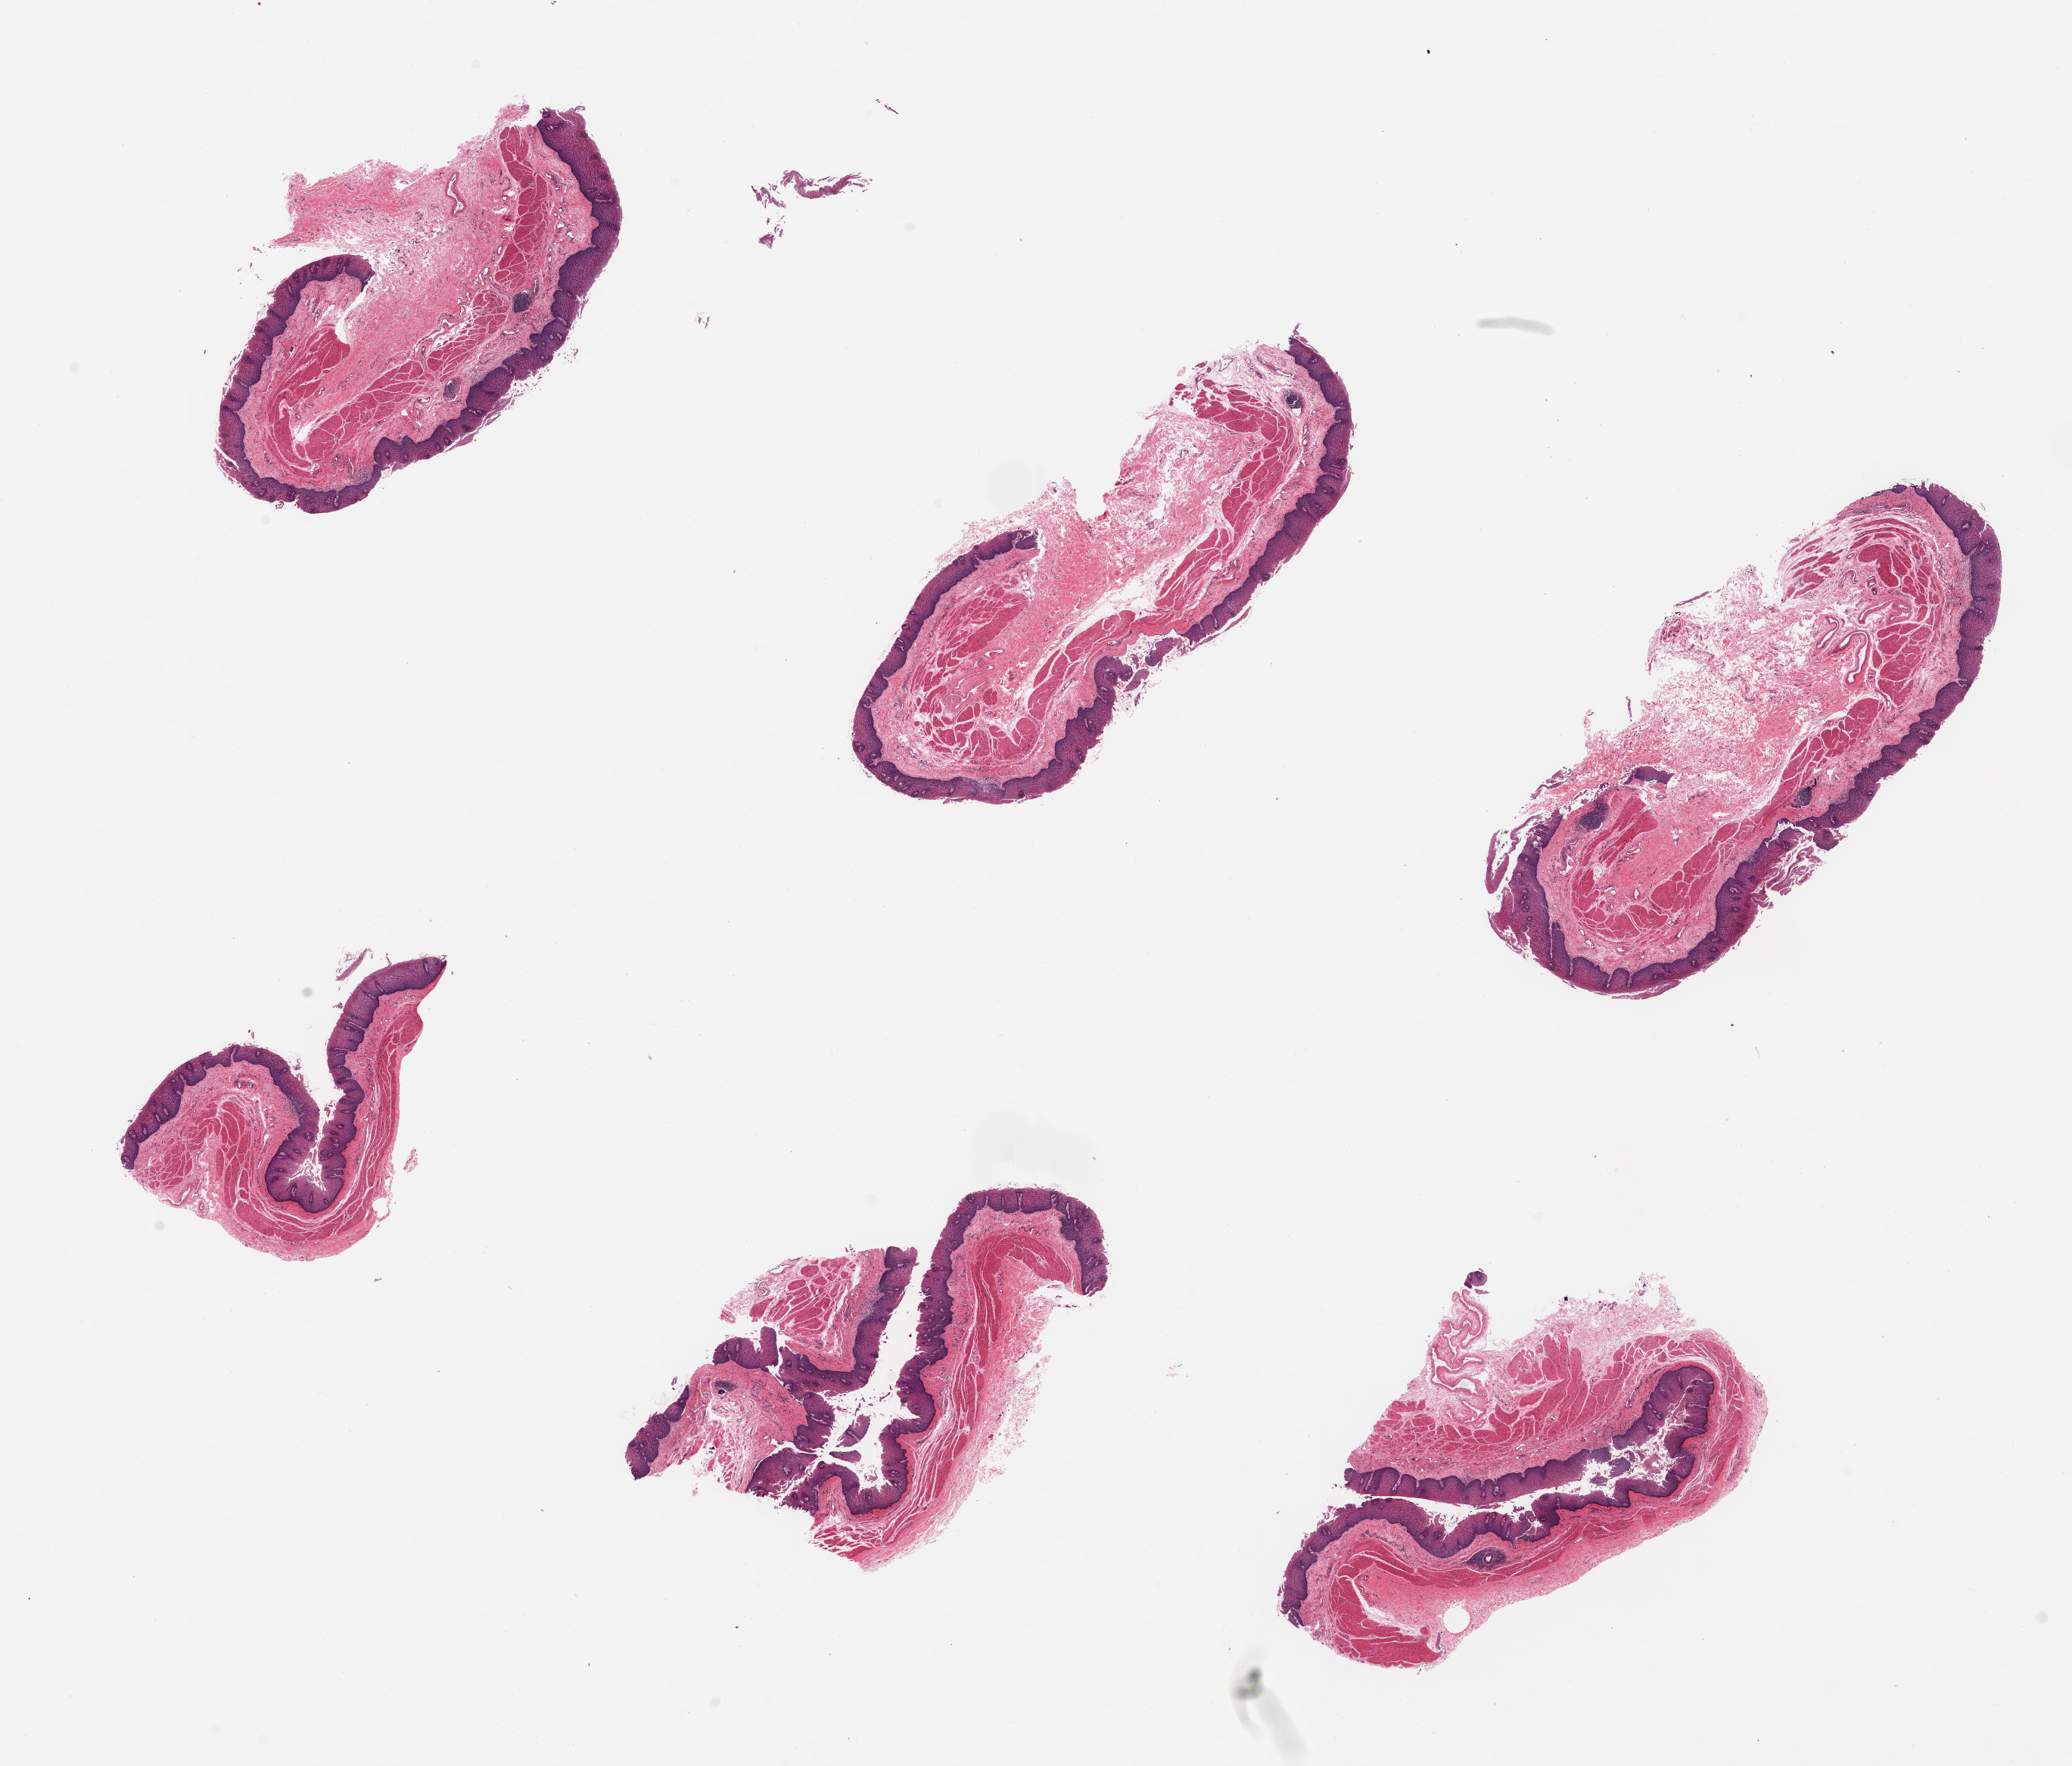
Whole-slide image, haematoxylin and eosin stain — whole scanned area (about 21.7 x 18.5 mm) shown as a low-resolution overview; PAXgene-fixed paraffin-embedded (PFPE) section; target tissue: esophageal mucous membrane; donor tissue sample. Donor: male.
* review note (as recorded): 6 pieces; small aggregates of lymphocytes in lamina propria; squamous epithelium measures 315.6um